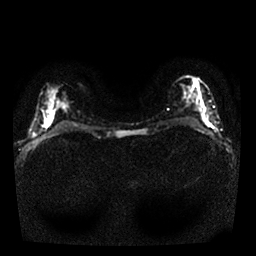
Breast MRI, one axial slice; slice 13 of 25 in the series (ordered by position); diffusion-weighted series; image 2 of 4 stored at this slice position (different b-values; order by instance number); 1.5 T; 4 mm slice thickness; 256 × 256 image matrix, field of view 320 × 320 mm. Female patient.
Structures marked on this image (manually delineated by an expert):
- tumour on diffusion-weighted imaging: bounding box [x1, y1, x2, y2] px = [203, 118, 208, 124]